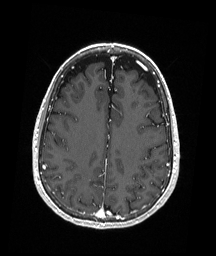
Brain MRI from a brain-tumour surgery series, one axial slice. Slice 76 of 192 in the series (ordered by position). T1-weighted post-contrast. 1 mm slice thickness. 216 × 256 image matrix, field of view 211 × 250 mm. From the clinical record (not read from this slice): histopathology: Astrocytoma; WHO grade: 3; IDH mutation: yes; tumour location: Right Parietal.
Outlined on this slice (manually delineated by an expert):
- tumour: bounding box <89,178,96,181> (left, top, right, bottom; pixels)